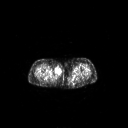
FDG PET of an extremity soft-tissue mass (from a PET/CT study), one axial slice. Slice 231 of 311 in the series (ordered by position). 3.27 mm slice thickness. 128 × 128 image matrix, field of view 700 × 700 mm. Female patient, age 78 years. From the clinical record (not read from this slice): histological type: leiomyosarcoma; grade: intermediate; site of the primary tumour: parascapusular.
Outlined on this slice (expert contour drawn on MRI and transferred to this co-registered scan by the dataset authors):
- gross tumour volume including surrounding oedema: bounding box <54,66,62,76> (left, top, right, bottom; pixels)
- gross tumour volume (mass): <54,66,62,76>